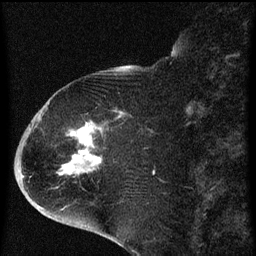
Breast MRI (dynamic contrast-enhanced), one sagittal slice. Position 23 of 60 along the scan axis. Dynamic contrast-enhanced series, image 2 of 4 at this slice position (ordered by acquisition). 1.5 T. TE 4.2 ms, TR 8 ms. 2 mm slice thickness. 256 × 256 image matrix. Female patient, age 71 years.
Outlined on this slice (semi-automatically segmented with operator editing):
- analysis volume of interest (the breast-tissue region the enhancement analysis was run in; not a lesion): bounding box (x1, y1, x2, y2) in pixels: (32, 86, 137, 205)
- tumour enhancement mask (voxels above the 70 % enhancement threshold inside the analysis volume of interest): (61, 114, 124, 175)